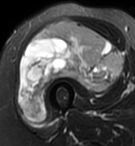
MRI of an extremity soft-tissue mass, one axial slice; position 45 of 95 along the scan axis; T2-weighted fat-saturated; MR volume resampled by the dataset authors to the PET/CT grid (not the native acquisition matrix); 135 × 146 image matrix. Female patient. From the clinical record (not read from this slice): histological type: pleiomorphic undifferentiated sarcoma; grade: high; site of the primary tumour: right quadricep.
Annotated regions visible in this slice (expert contour drawn on MRI and transferred to this co-registered scan by the dataset authors):
- gross tumour volume including surrounding oedema: bounding box (x1, y1, x2, y2) in pixels: (19, 20, 122, 121)
- gross tumour volume (mass): (19, 20, 122, 121)